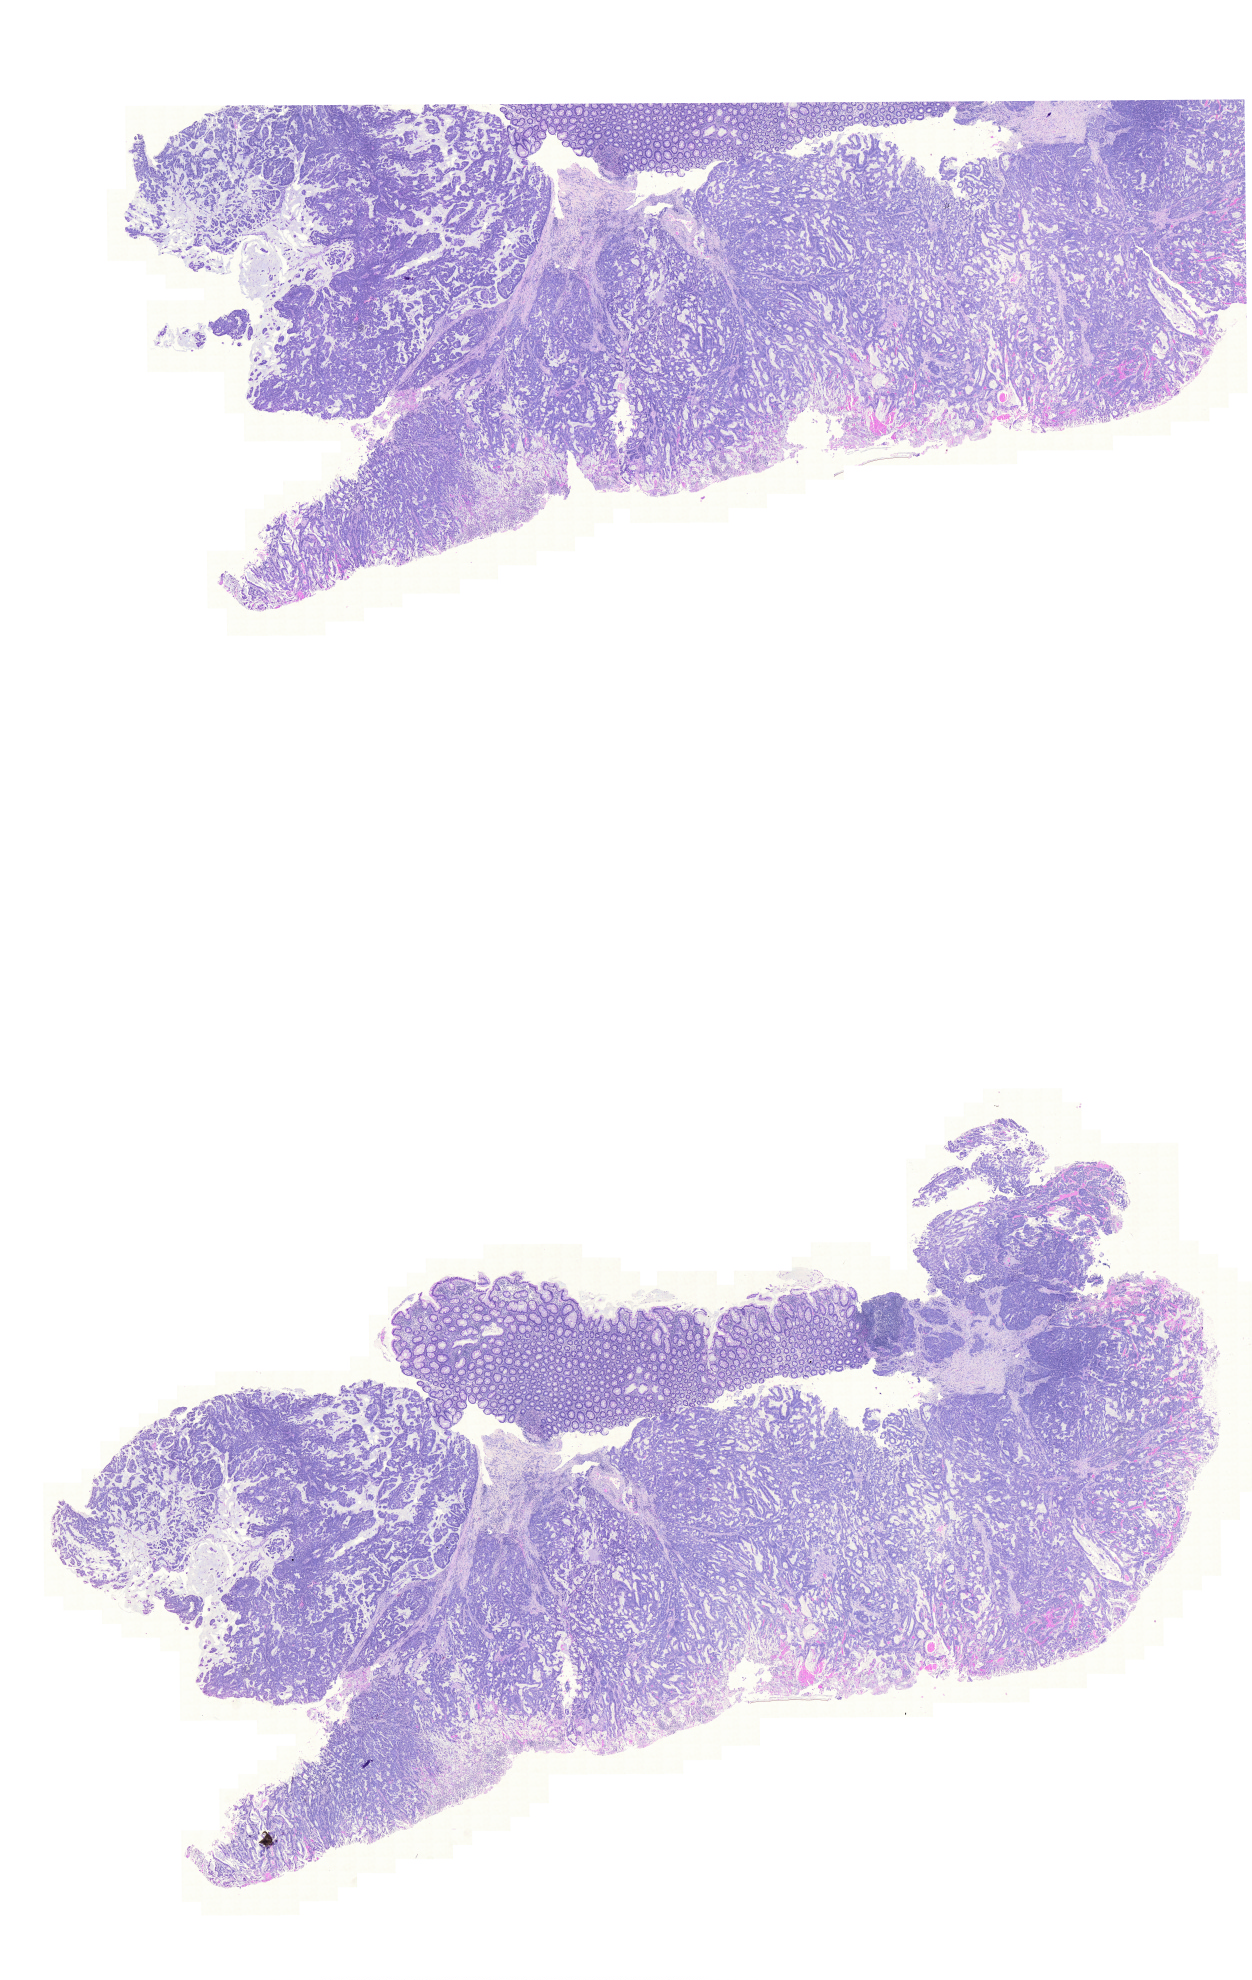
H&E-stained whole-slide image — whole scanned area (about 18.6 x 29.5 mm, acquisition: 20x scan) shown as a low-resolution overview; formalin-fixed paraffin-embedded (FFPE) diagnostic section; sample: primary tumour, colon. Male, age 80 years at initial diagnosis.
- lymph nodes positive (case pathology): 2 of 24 examined
- TNM: T4 N1 M0
- diagnosis: Mucinous adenocarcinoma (ascending colon)
- AJCC pathologic stage: IIIB (6th edition)